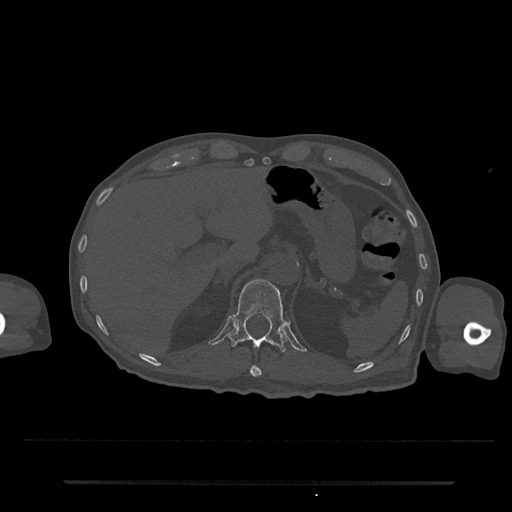
CT including the spine, one axial slice. Position 202 of 797 along the scan axis. Reconstruction kernel Br40s/3. Bone window (W 1800 / L 400 HU). 0.5 mm slice thickness. 512 × 512 image matrix. Male patient, age 74 years. Case-level facts recorded for this patient, not image findings: primary cancer: prostate.
Annotated regions visible in this slice (semi-automatic segmentation, software-assisted and operator-edited):
- T11 vertebra: bounding box (x1, y1, x2, y2) in pixels: (250, 366, 262, 377)
- T12 vertebra: (229, 279, 287, 352)